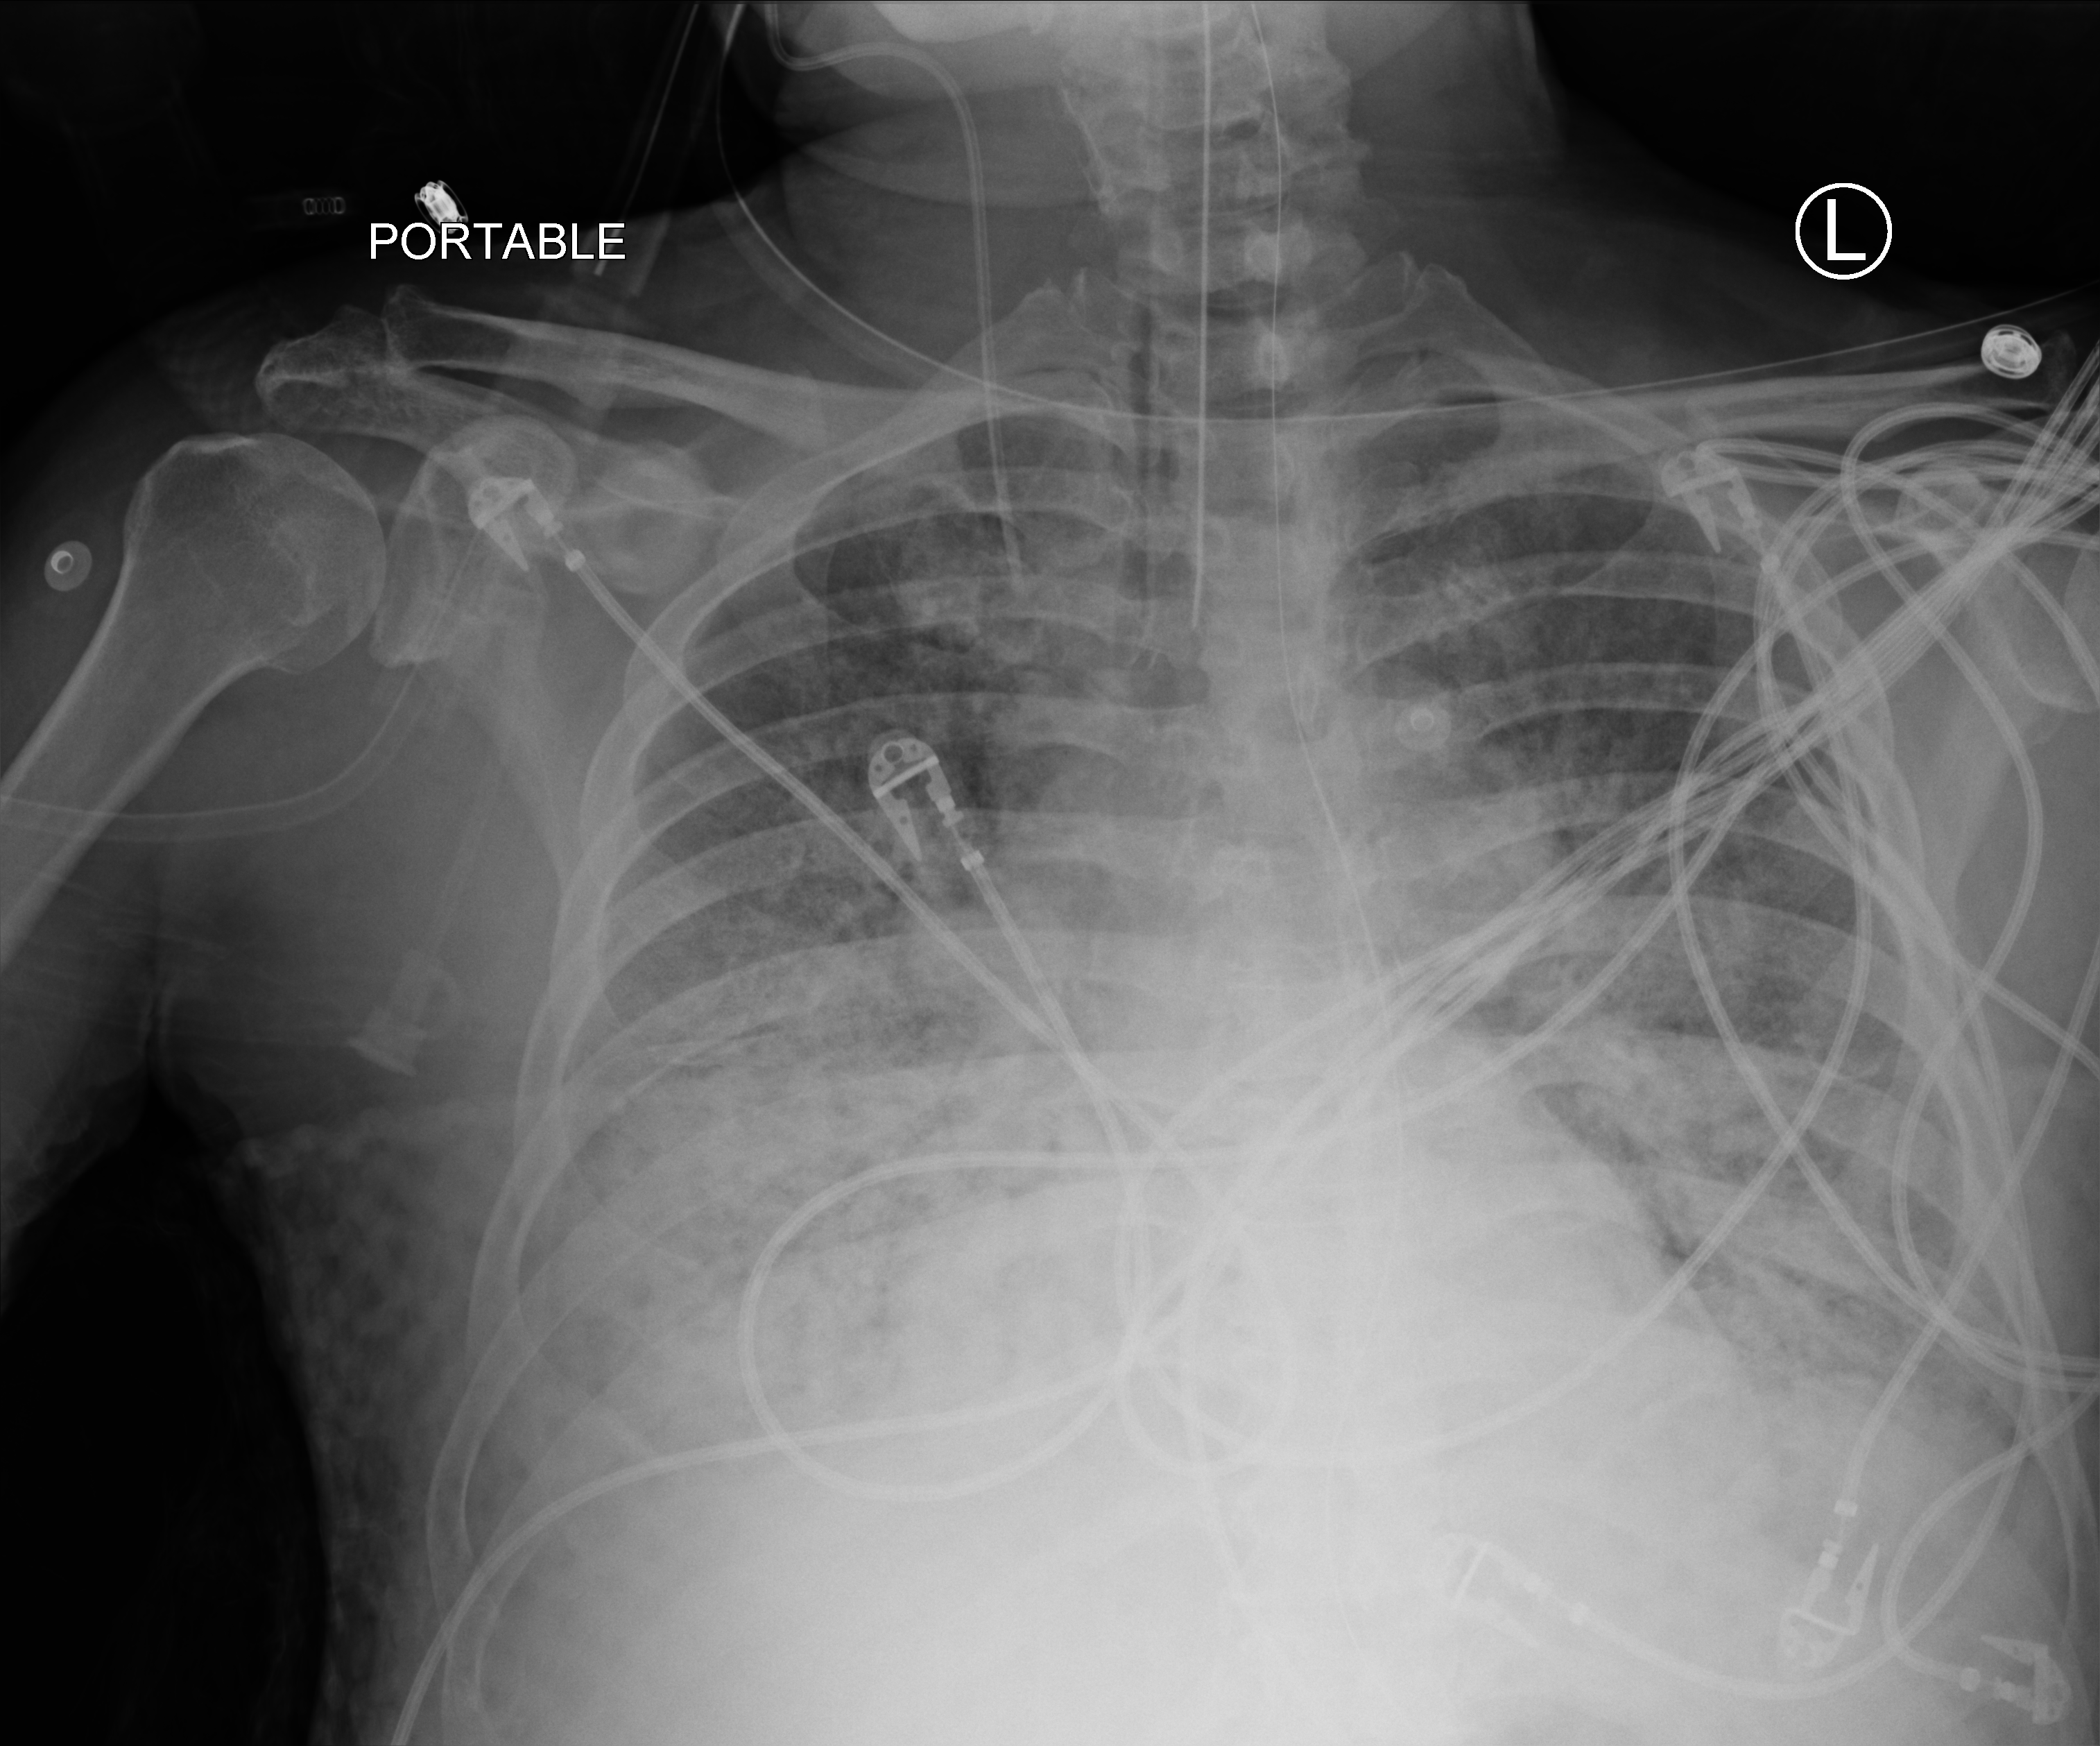
Portable chest radiograph; anteroposterior (AP) projection. Patient hospitalised with COVID-19; male, aged 60–74 years.
Hospital-stay facts (about this admission, not read from this image; timing relative to this image not recorded):
- smoking status (admission record): never
- mechanically ventilated during this hospital stay: yes
- diabetes (admission record): no